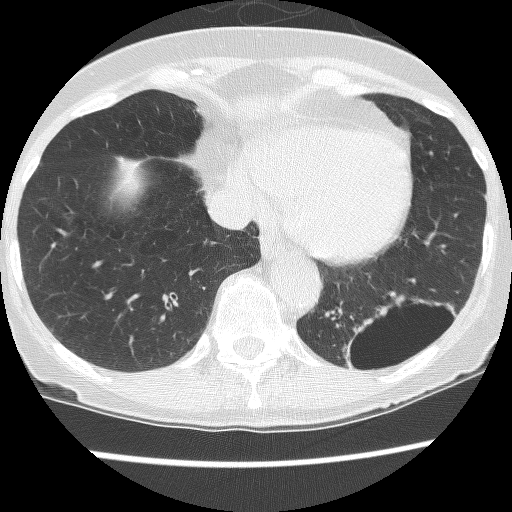
Low-dose screening chest CT, axial slice; third screening round (two years after baseline); lung window (W 1500 / L -600 HU); lung (sharp) reconstruction kernel (BONE); 120 kVp; slice 95 of 130 in the series. Female, age 61 years at enrolment. Current smoker at enrolment.
Lesion marked by an expert reader, bounding box (x1, y1, x2, y2) in pixels: (333, 293, 443, 387). The screening reader recorded 2 non-calcified nodules or masses ≥4 mm on this exam (left lower lobe, left lower lobe); which of them this box marks is not recorded. Official screen result: positive, no significant change: stable abnormalities potentially related to lung cancer, unchanged since the prior screening exam. Lung cancer was diagnosed 166 days after this screen: non-small cell carcinoma, left lower lobe, poorly differentiated (G3), stage IB (AJCC 6th edition), 100 mm at pathology.